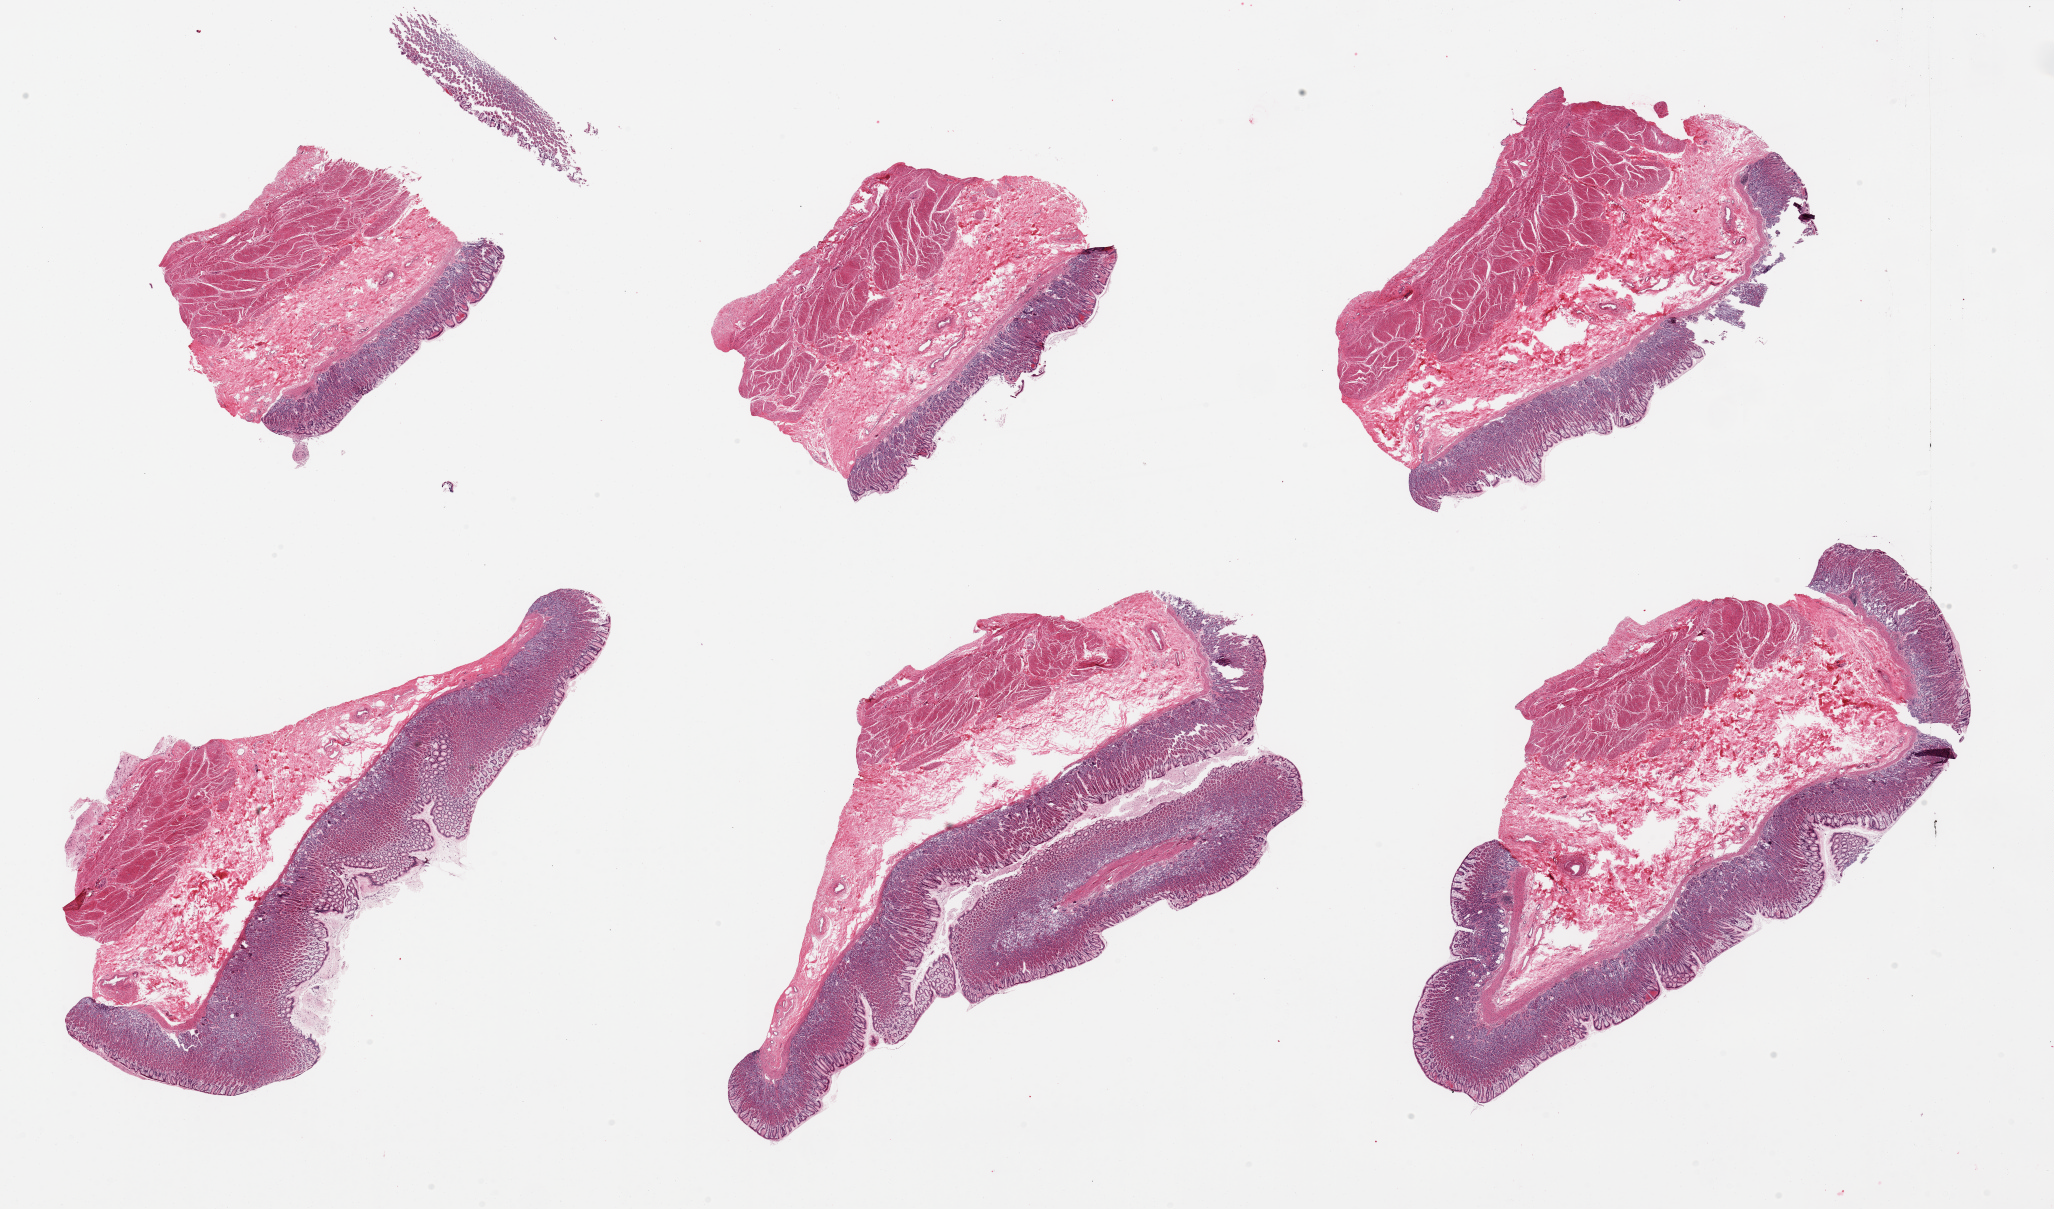
Digitized H&E-stained section, a low-resolution overview of the entire scanned area, about 32.5 x 19.1 mm (from a 20x scan). PAXgene-fixed, paraffin-embedded tissue. Target tissue: stomach. Tissue donor sample.
* pathologist's review note for this sample: 6 pieces; full thickness sections, some superficial hemorrhage and focal basal dilatation of glands